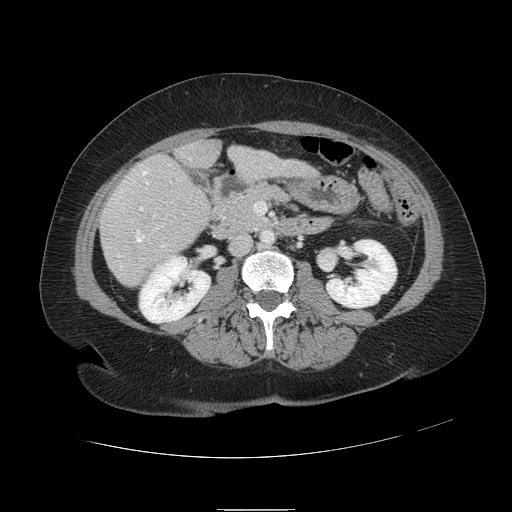
Contrast-enhanced abdominal CT, one axial slice. Slice 32 of 121 in the series (ordered by position). 120 kVp. Intravenous contrast given. Soft-tissue window (W 400 / L 40 HU). 2.5 mm slice thickness. 512 × 512 image matrix, field of view 400 × 400 mm. Female patient, age 52 years. From the clinical record (not read from this slice): diagnosis: colorectal cancer liver metastases, imaged before liver resection; multiple liver metastases: yes; largest metastasis: 6.3 cm; disease in both lobes: no.
Structures marked on this image (outlined manually by an expert reader):
- hepatic veins: bounding box <121,167,271,268> (left, top, right, bottom; pixels)
- liver: <100,141,311,286>
- planned liver remnant (the part of the liver to remain after resection): <177,141,311,178>
- portal vein (with intrahepatic branches): <139,207,143,211>